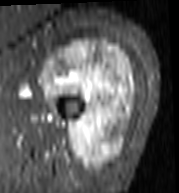
MRI of an extremity soft-tissue mass, one axial slice. Position 71 of 103 along the scan axis. STIR. MR volume resampled by the dataset authors to the PET/CT grid (not the native acquisition matrix). 179 × 193 image matrix, field of view 175 × 188 mm. Female patient. From the clinical record (not read from this slice): histological type: undifferentiated – high grade; grade: high; site of the primary tumour: left thigh.
Structures marked on this image (expert contour drawn on MRI and transferred to this co-registered scan by the dataset authors):
- gross tumour volume including surrounding oedema: bounding box (x1, y1, x2, y2) in pixels: (41, 39, 137, 170)
- gross tumour volume (mass): (41, 39, 135, 170)